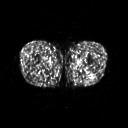
FDG PET of an extremity soft-tissue mass (from a PET/CT study), one axial slice; position 227 of 267 along the scan axis; 128 × 128 image matrix, field of view 500 × 500 mm. Male patient, age 27 years. Case-level facts recorded for this patient, not image findings: histological type: extraskeletal osteosarcoma; grade: high; site of the primary tumour: left adductur.
Outlined on this slice (expert contour drawn on MRI and transferred to this co-registered scan by the dataset authors):
- gross tumour volume (mass): bounding box (x1, y1, x2, y2) in pixels: (68, 61, 92, 77)